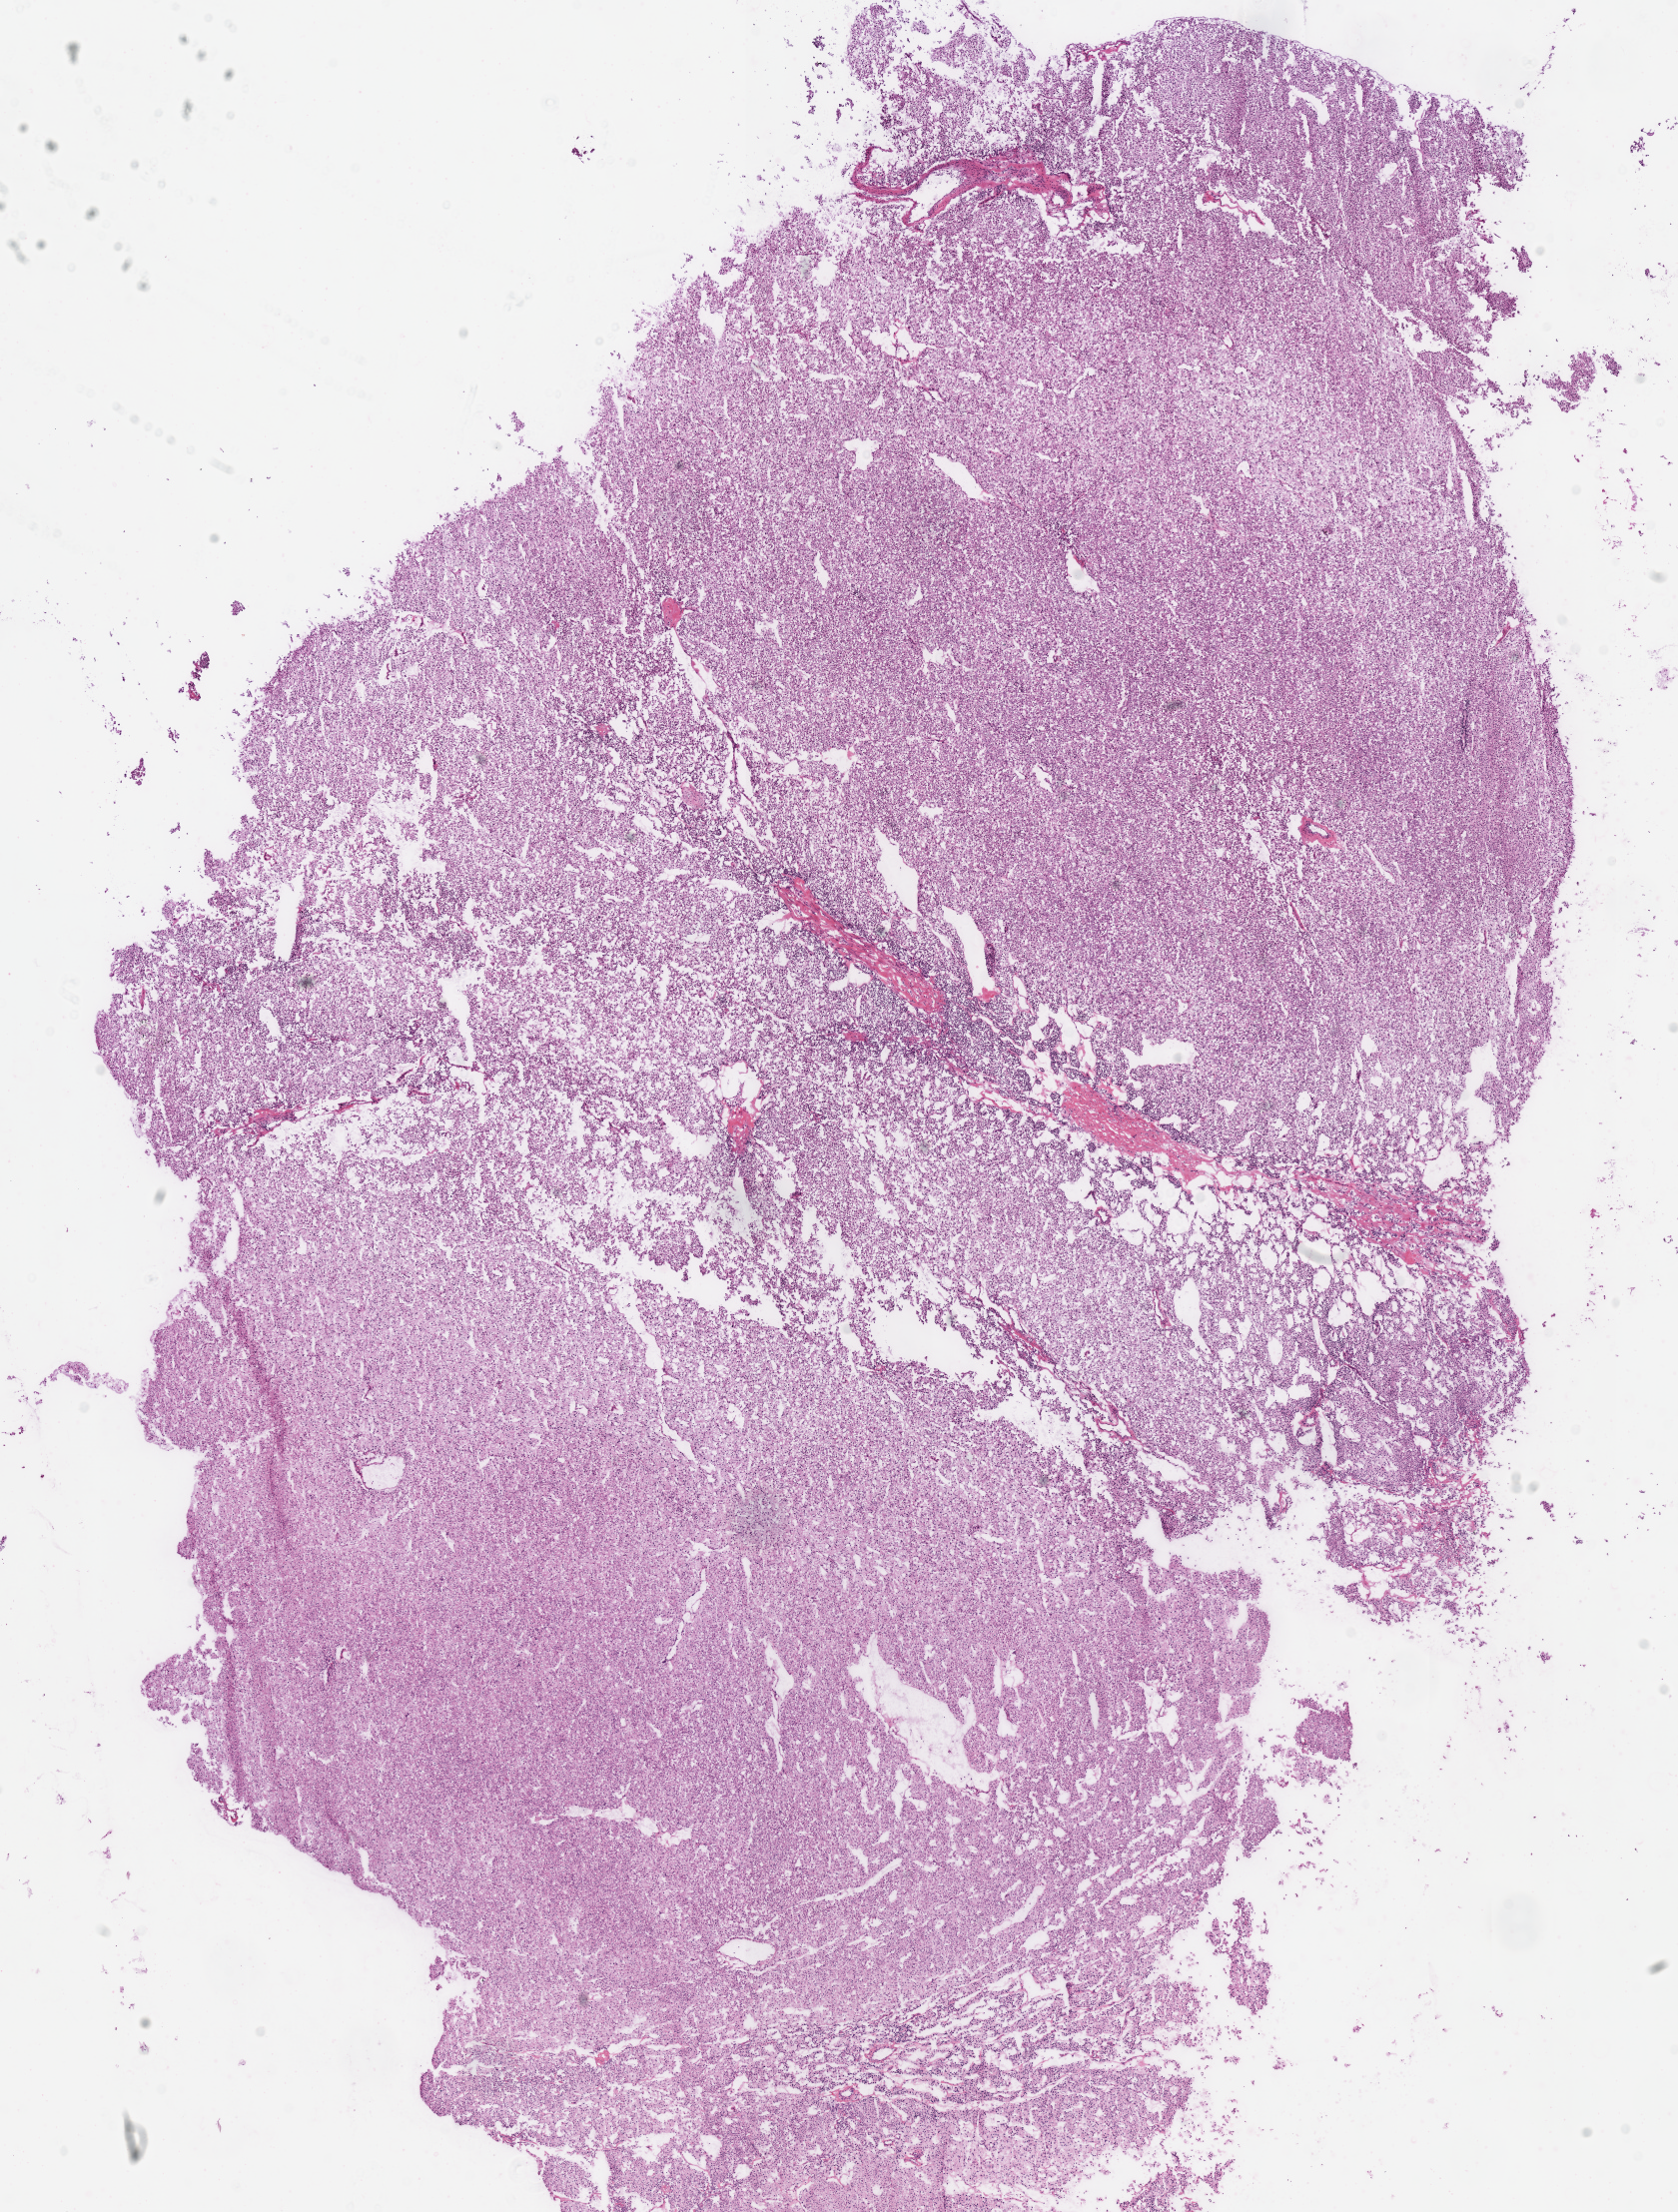
Digitized H&E tissue section (whole slide) — a low-resolution overview of the entire scanned area, about 13.2 x 17.4 mm (acquisition: 40x scan), frozen section from the top of the tissue portion, sample: primary tumour, kidney. Male, age 38 years at initial diagnosis. Slide review estimates, as recorded: tumour cells 90%, tumour nuclei 90%, normal cells 0%, stromal cells 10%, necrosis 0%.
TNM: T2 NX MX. Histologic diagnosis: Renal cell carcinoma, chromophobe type. AJCC pathologic stage: II (6th edition).